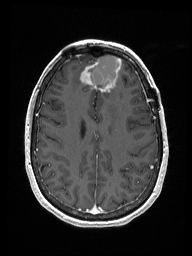
Brain MRI from a brain-tumour surgery series, one axial slice; T1-weighted post-contrast; 1 mm slice thickness; 192 × 256 image matrix. From the clinical record (not read from this slice): histopathology: Metastastic Carcinoma from Breast primary; tumour location: Right Frontal.
Structures marked on this image (outlined manually by an expert reader):
- previous resection cavity: bounding box (x1, y1, x2, y2) in pixels: (89, 55, 120, 89)